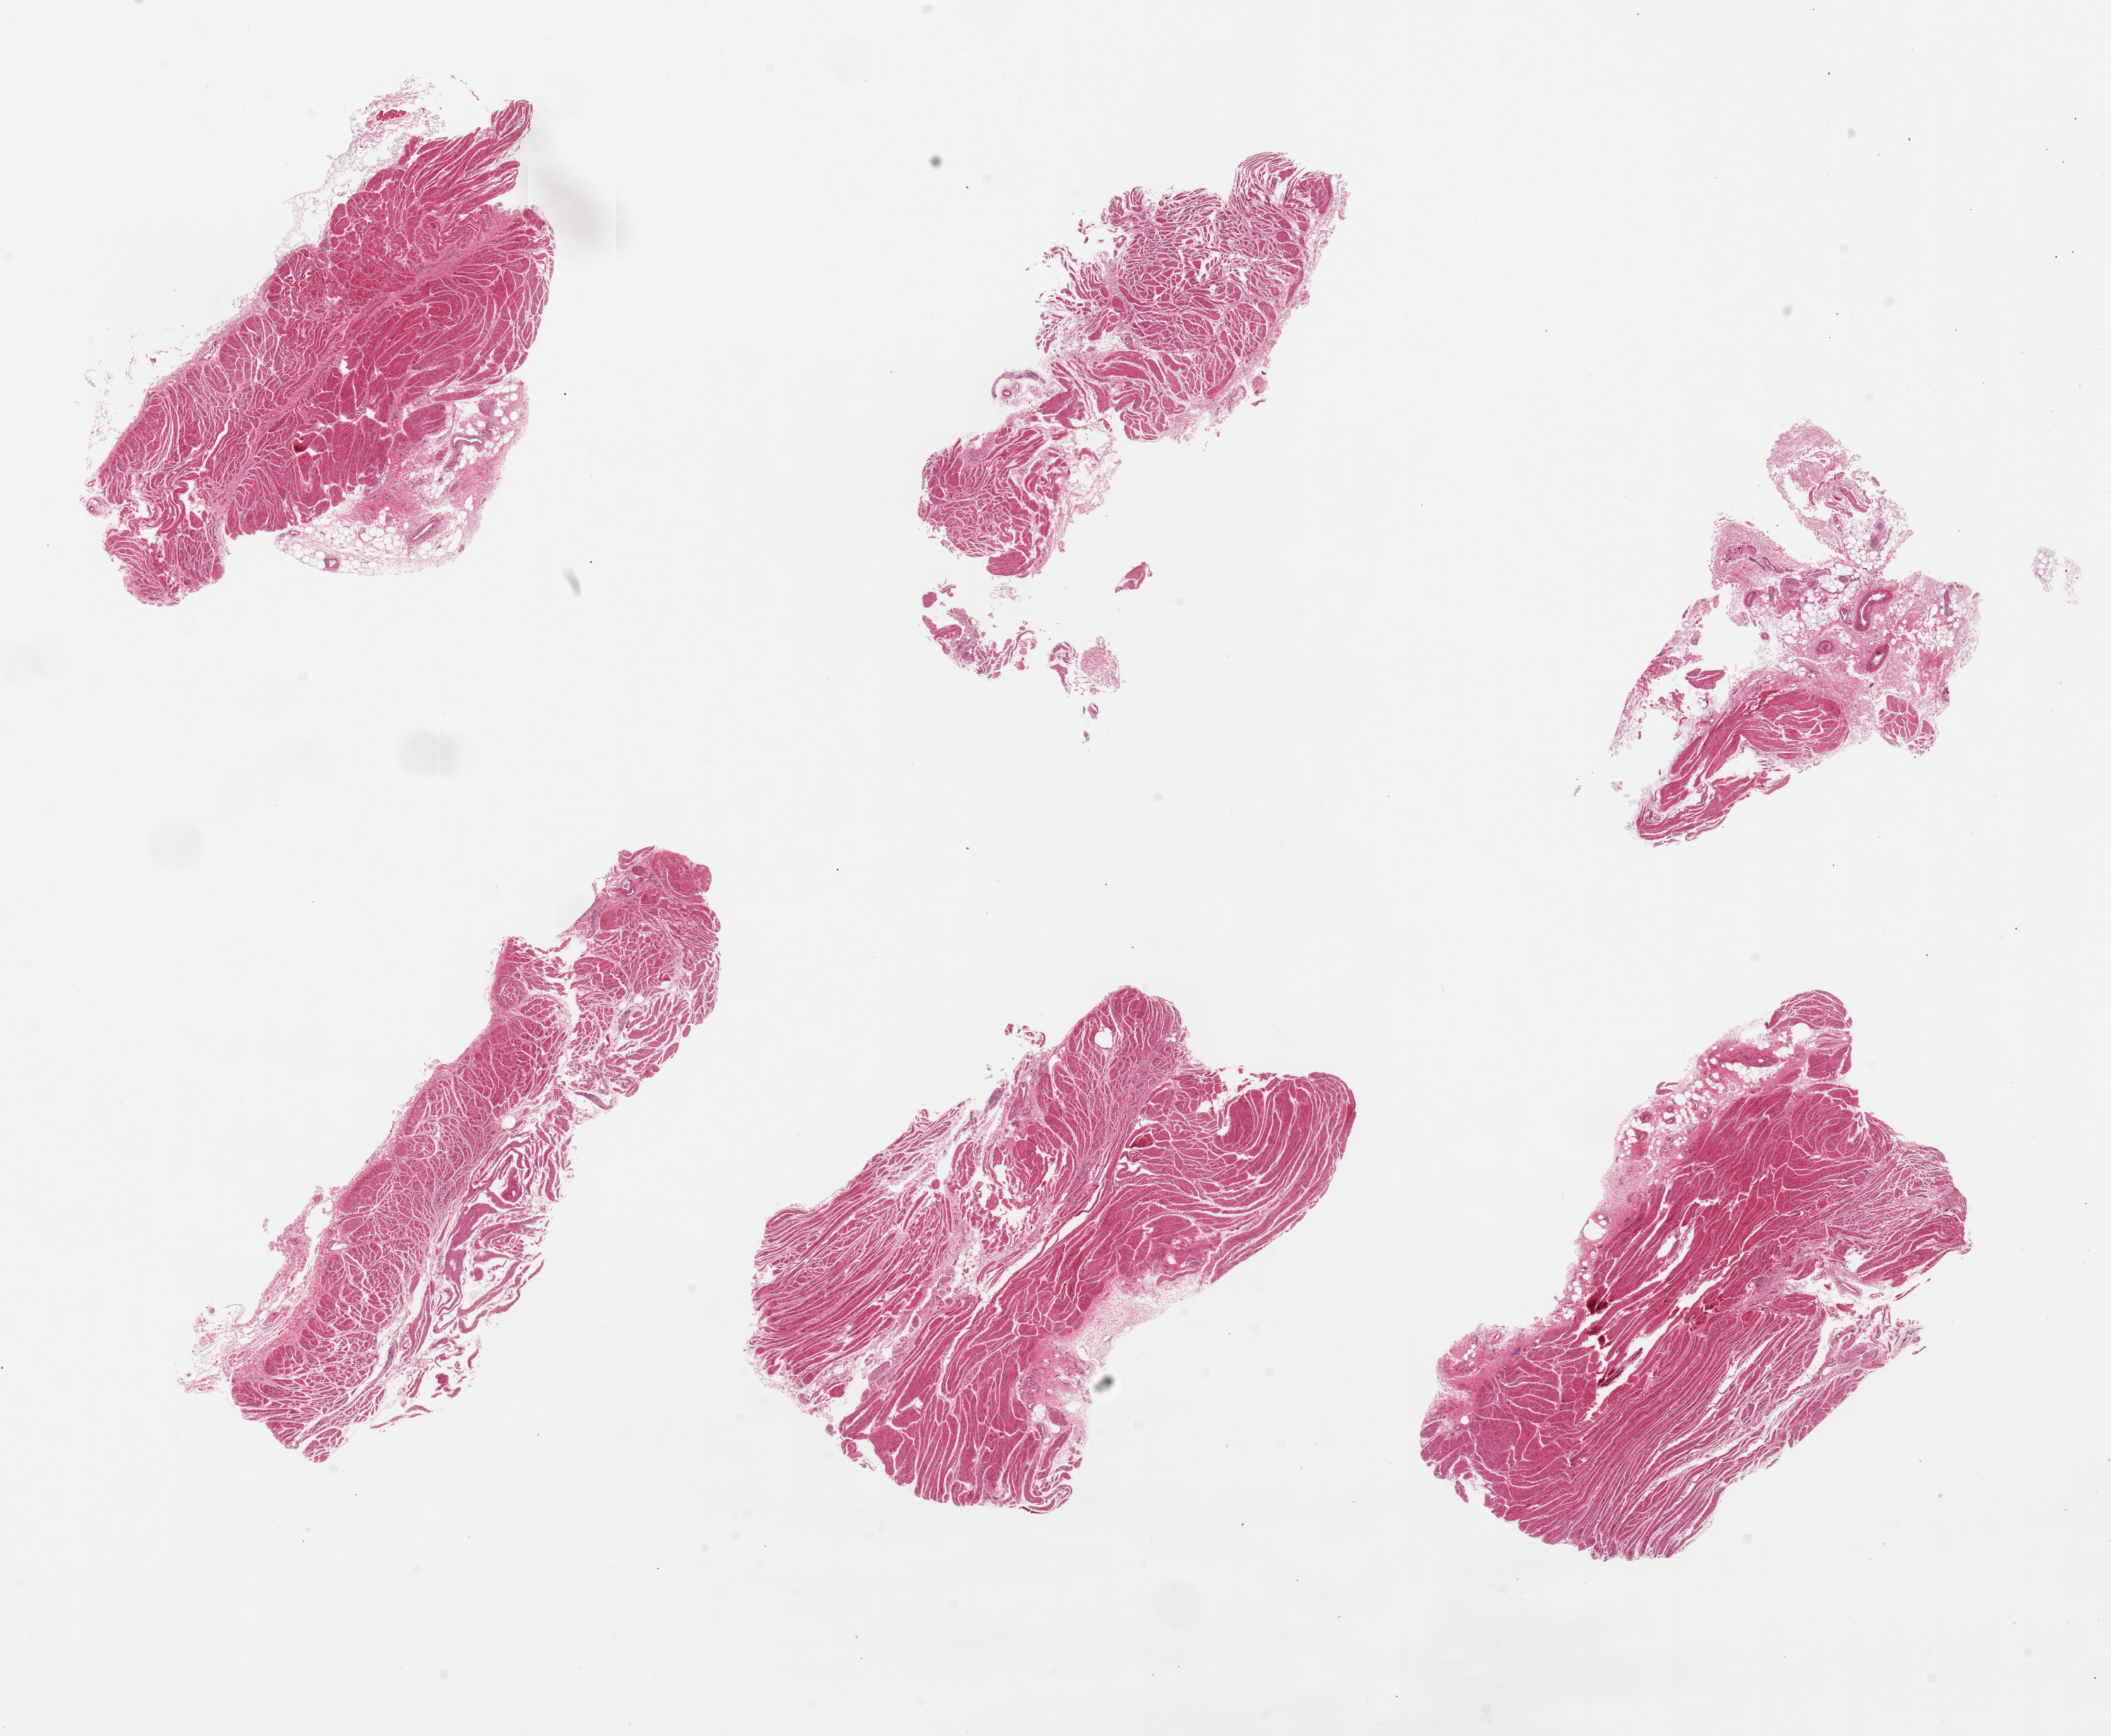
Whole-slide image, hematoxylin and eosin (H&E) stain — shown as a low-resolution overview of the whole scanned area (about 23.6 x 19.4 mm), PAXgene-fixed paraffin-embedded (PFPE) section, section of gastroesophageal junction (target tissue), tissue donor sample. Donor: female.
Reviewer comment on this tissue sample: 6 pieces, up to 8x3mm. 1 piece 60% fibroadipose stroma; others are largely muscle (target).